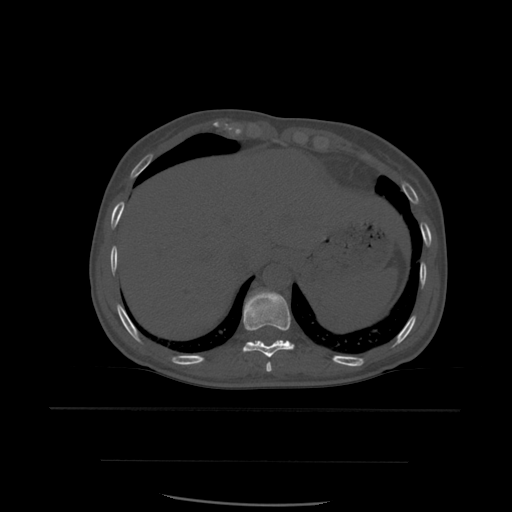
CT including the spine, one axial slice; slice 314 of 574 in the series (ordered by position); bone window (W 1800 / L 400 HU); 1.25 mm slice thickness; 512 × 512 image matrix, field of view 392 × 392 mm. Patient age 48 years. From the clinical record (not read from this slice): primary cancer: lung; vertebrae with lytic lesions (as recorded): T11.
Outlined on this slice (semi-automatic segmentation, software-assisted and operator-edited):
- T10 vertebra: box from (x=242, y=291) to (x=295, y=358) px
- T11 vertebra: (x=255, y=341)–(x=266, y=346)
- T9 vertebra: (x=266, y=362)–(x=272, y=372)